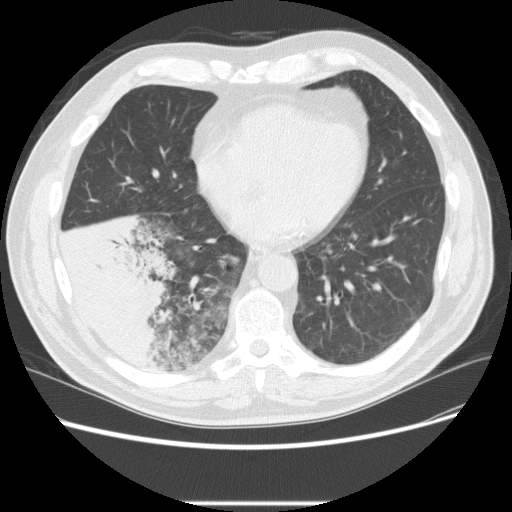
Low-dose screening chest CT, one axial slice. Position 86 of 233 along the scan axis. 120 kVp. Lung window (W 1500 / L -600 HU). 2.5 mm slice thickness. 512 × 512 image matrix, field of view 380 × 380 mm.
Outlined on this slice (manually delineated by an expert):
- lesion 3 (tumor, lower lobe of right lung): bounding box <58,211,177,367> (left, top, right, bottom; pixels)